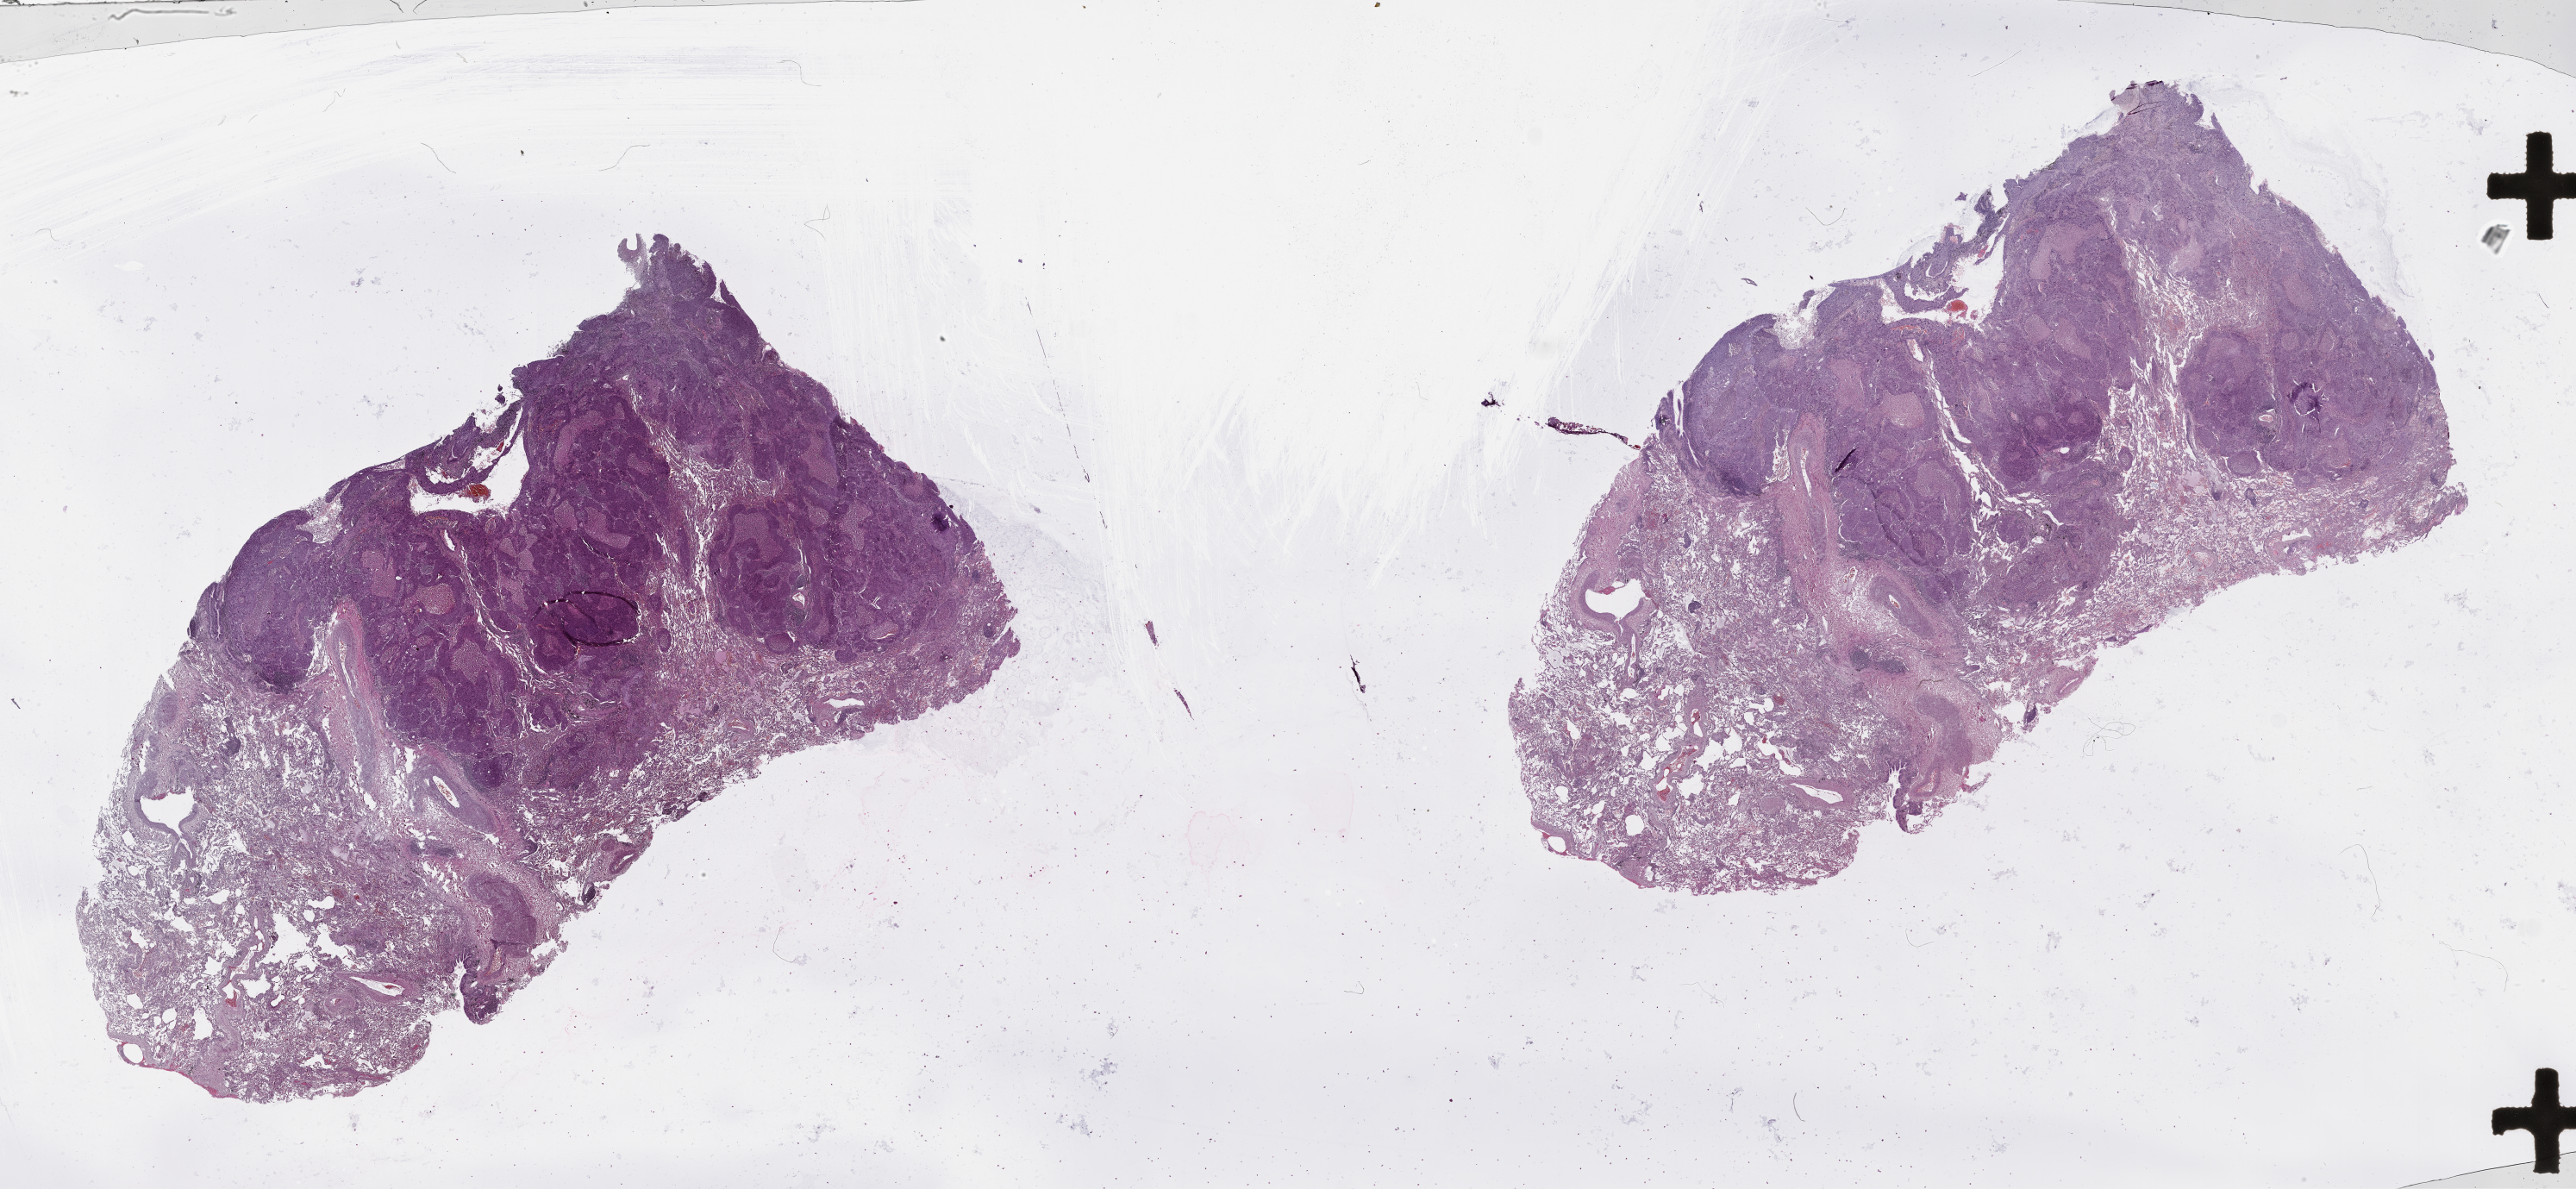
Digitized H&E tissue section (whole slide) — a low-resolution overview of the entire scanned area, about 48.1 x 22.2 mm, tumour tissue sample, lung. 75-year-old male patient.
* patient diagnosis (cohort enrolment): squamous cell carcinoma (lung)